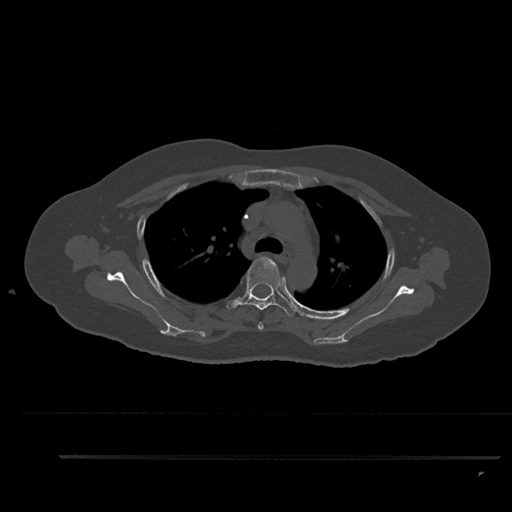
CT including the spine, one axial slice. Slice 650 of 797 in the series (ordered by position). Reconstruction kernel Br40s/3. 120 kVp. Bone window (W 1800 / L 400 HU). 0.5 mm slice thickness. 512 × 512 image matrix, field of view 408 × 408 mm. Female patient, age 44 years. From the clinical record (not read from this slice): primary cancer: renal.
Annotated regions visible in this slice (semi-automatic segmentation, software-assisted and operator-edited):
- T3 vertebra: box from (x=258, y=322) to (x=264, y=330) px
- T4 vertebra: (x=226, y=257)–(x=296, y=317)